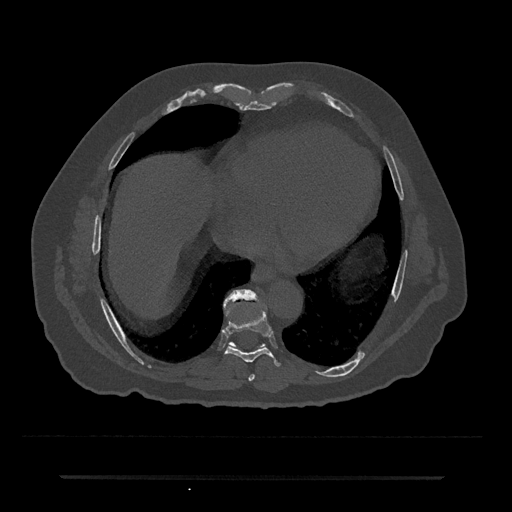
CT including the spine, one axial slice. Slice 320 of 797 in the series (ordered by position). Reconstruction kernel Br40s/3. Bone window (W 1800 / L 400 HU). 0.5 mm slice thickness. 512 × 512 image matrix, field of view 437 × 437 mm. Patient: male, 69 years. Case-level facts recorded for this patient, not image findings: primary cancer: prostate.
Annotated regions visible in this slice (semi-automatically segmented with operator editing):
- T7 vertebra: bounding box (x1, y1, x2, y2) in pixels: (248, 374, 255, 381)
- T8 vertebra: (225, 310, 281, 366)
- T9 vertebra: (226, 289, 257, 307)